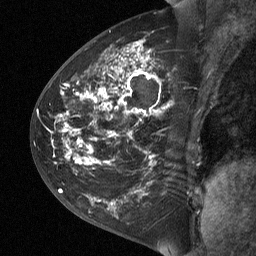
Breast MRI (dynamic contrast-enhanced), one sagittal slice; slice 29 of 64 in the series (ordered by position); dynamic contrast-enhanced study with each time point stored as its own series, time point 2 of 3 at this slice position (early post-contrast, ordered by acquisition time); 1.5 T; TE 4.8 ms, TR 27 ms; 2 mm slice thickness; 256 × 256 image matrix, field of view 200 × 200 mm. Female patient, age 42 years. Case-level facts recorded for this patient, not image findings: setting: breast cancer imaged before/during neoadjuvant chemotherapy; receptor status: triple-negative.
Outlined on this slice (semi-automatic segmentation, software-assisted and operator-edited):
- analysis volume of interest (the breast-tissue region the enhancement analysis was run in; not a lesion): bounding box <43,29,201,190> (left, top, right, bottom; pixels)
- tumour enhancement mask (voxels above the 90 % enhancement threshold inside the analysis volume of interest): <59,44,158,163>